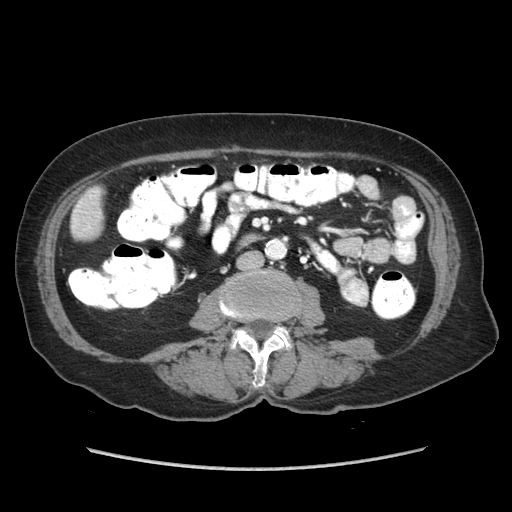
Contrast-enhanced abdominal CT (liver protocol), one axial slice; position 7 of 89 along the scan axis; reconstruction kernel STANDARD; soft-tissue window (W 400 / L 40 HU); 512 × 512 image matrix, field of view 360 × 360 mm. Case-level facts recorded for this patient, not image findings: diagnosis: hepatocellular carcinoma (patient treated with transarterial chemoembolisation; whether this scan precedes or follows treatment is not stated here); TNM stage (as recorded): Stage-IIIA; Child-Pugh class: A; tumour differentiation: well differentiated; tumour nodularity: multinodular.
Outlined on this slice (semi-automatically segmented with operator editing):
- liver parenchyma outside the tumour (the mass and vessels are separate outlines, so this box may not span the whole liver): bounding box [x1, y1, x2, y2] px = [70, 186, 102, 238]